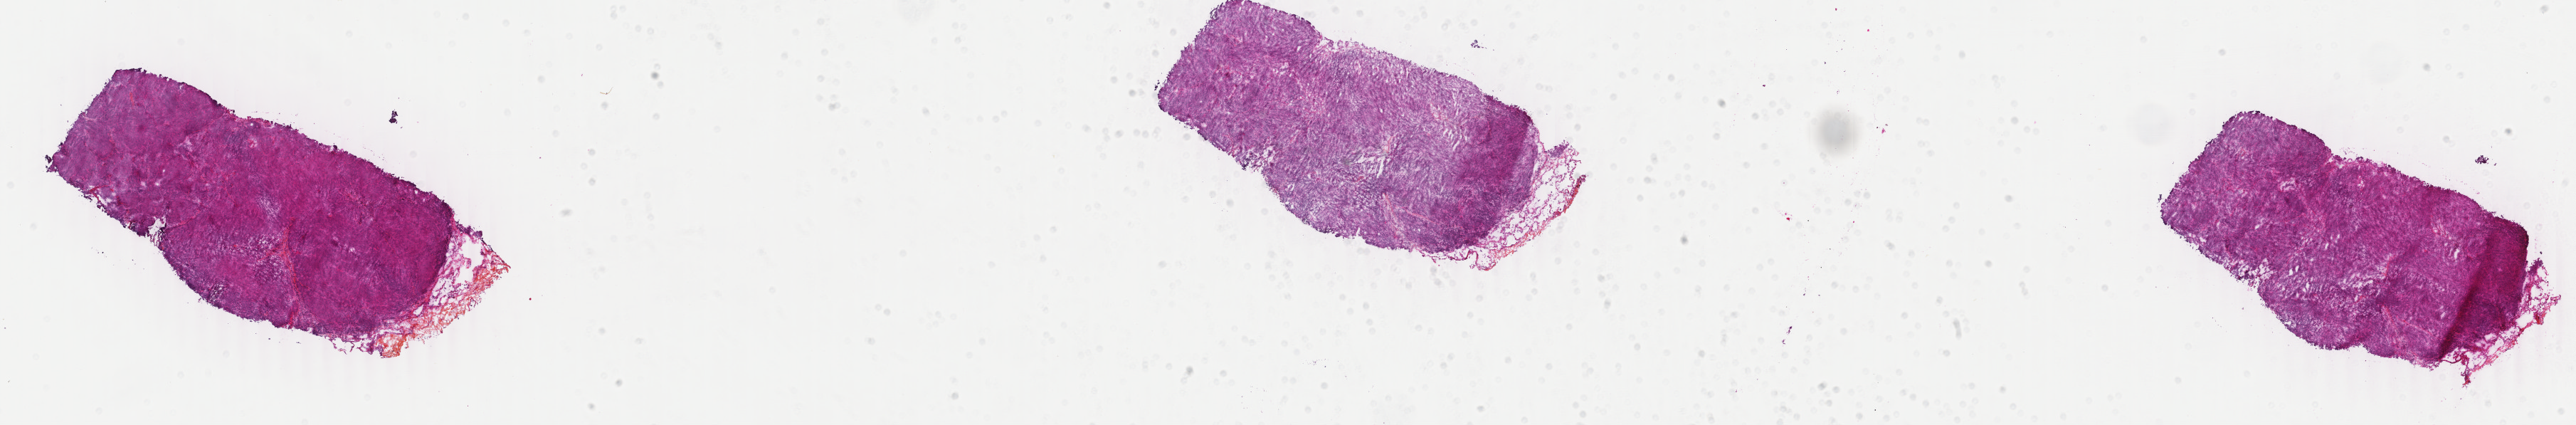
H&E-stained whole-slide image — a low-resolution overview of the entire scanned area, about 28.8 x 4.7 mm (acquisition: 40x scan); frozen section; primary tumour sample from the thymus. Patient: male, age at initial diagnosis 64 years. Composition of this section per pathologist review: tumour cells 99%, tumour nuclei 99%, normal cells 0%, stromal cells 1%, necrosis 0%. Inflammatory infiltration, as recorded: lymphocyte infiltration 0%, monocyte infiltration 0%, neutrophil infiltration 0%.
Pathologic diagnosis: Thymoma, type B3, malignant.